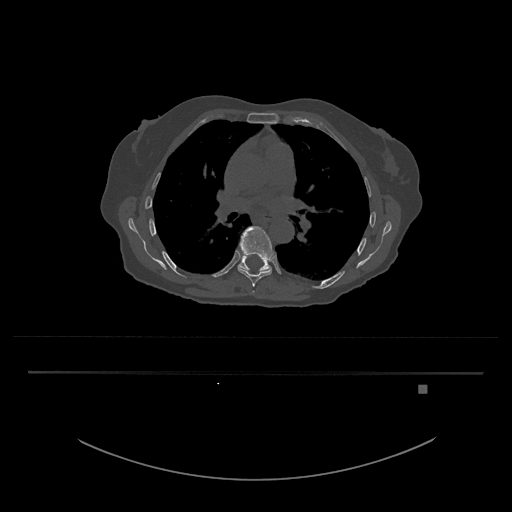
CT including the spine, one axial slice; position 790 of 797 along the scan axis; reconstruction kernel Br40s/3; bone window (W 1800 / L 400 HU); 512 × 512 image matrix. Female patient, age 57 years. Case-level facts recorded for this patient, not image findings: primary cancer: cervical.
Outlined on this slice (semi-automatically segmented with operator editing):
- T8 vertebra: bounding box [x1, y1, x2, y2] px = [237, 226, 275, 287]
- T9 vertebra: [238, 255, 272, 272]